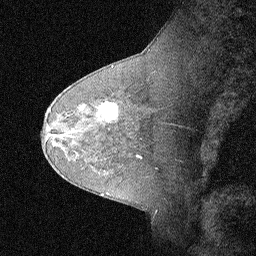
Breast MRI (dynamic contrast-enhanced), one sagittal slice; slice 44 of 64 in the series (ordered by position); dynamic contrast-enhanced study with each time point stored as its own series, time point 2 of 3 at this slice position (early post-contrast, ordered by acquisition time); 1.5 T; TE 4.5 ms, TR 11 ms; 2.06 mm slice thickness; 256 × 256 image matrix, field of view 200 × 200 mm. Patient: female, 62 years. From the clinical record (not read from this slice): setting: breast cancer imaged before/during neoadjuvant chemotherapy; receptor status: HR-positive, HER2-negative.
Outlined on this slice (semi-automatic segmentation, software-assisted and operator-edited):
- analysis volume of interest (the breast-tissue region the enhancement analysis was run in; not a lesion): box from (x=91, y=93) to (x=124, y=129) px
- tumour enhancement mask (voxels above the 90 % enhancement threshold inside the analysis volume of interest): (x=99, y=102)–(x=118, y=121)